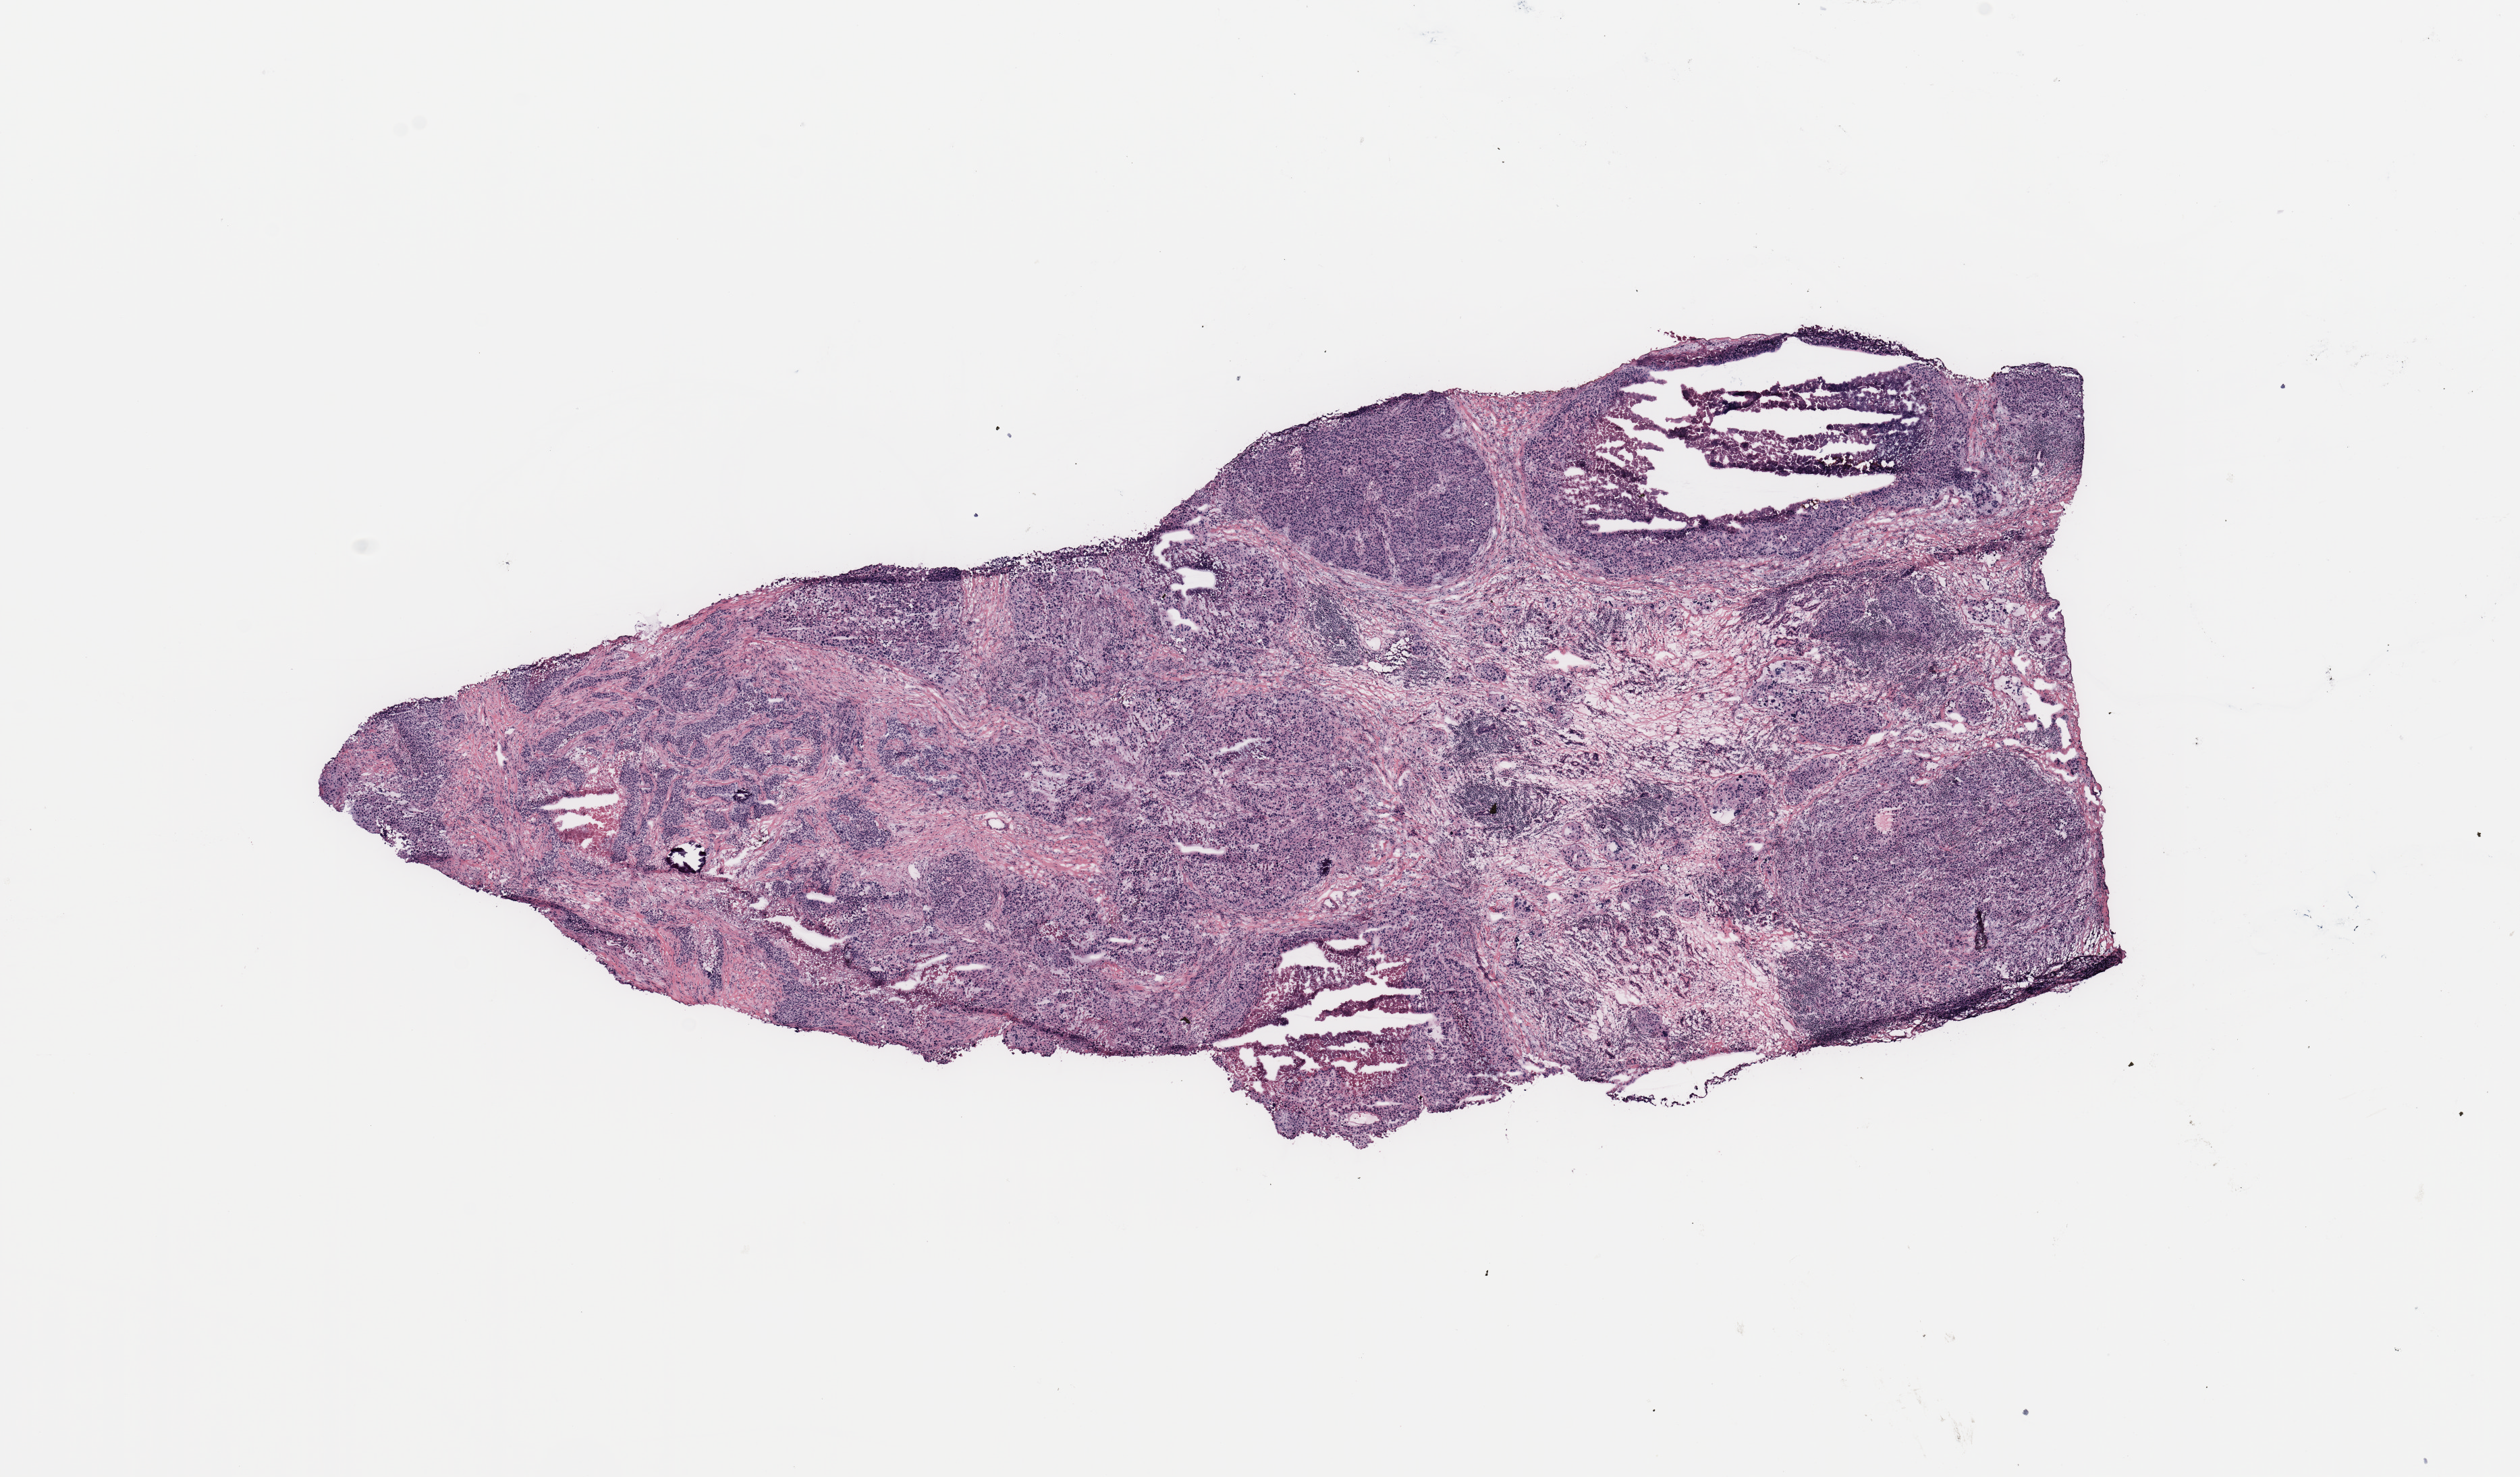
Hematoxylin and eosin (H&E) stained whole-slide image, a low-resolution overview of the entire scanned area, about 14.8 x 8.7 mm (from a 20x scan). Breast, tumour tissue. 40-year-old female patient.
AJCC pathologic stage: IIB. Histologic diagnosis: Infiltrating duct carcinoma, NOS.